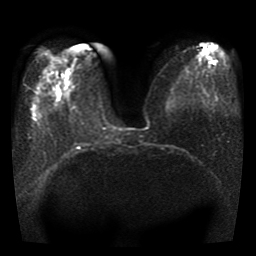
Breast MRI, one axial slice; slice 12 of 41 in the series (ordered by position); diffusion-weighted series; image 2 of 4 stored at this slice position (different b-values; order by instance number); 1.5 T; 256 × 256 image matrix, field of view 330 × 330 mm. Female patient.
Structures marked on this image (manually delineated by an expert):
- tumour on diffusion-weighted imaging: bounding box <58,88,62,96> (left, top, right, bottom; pixels)